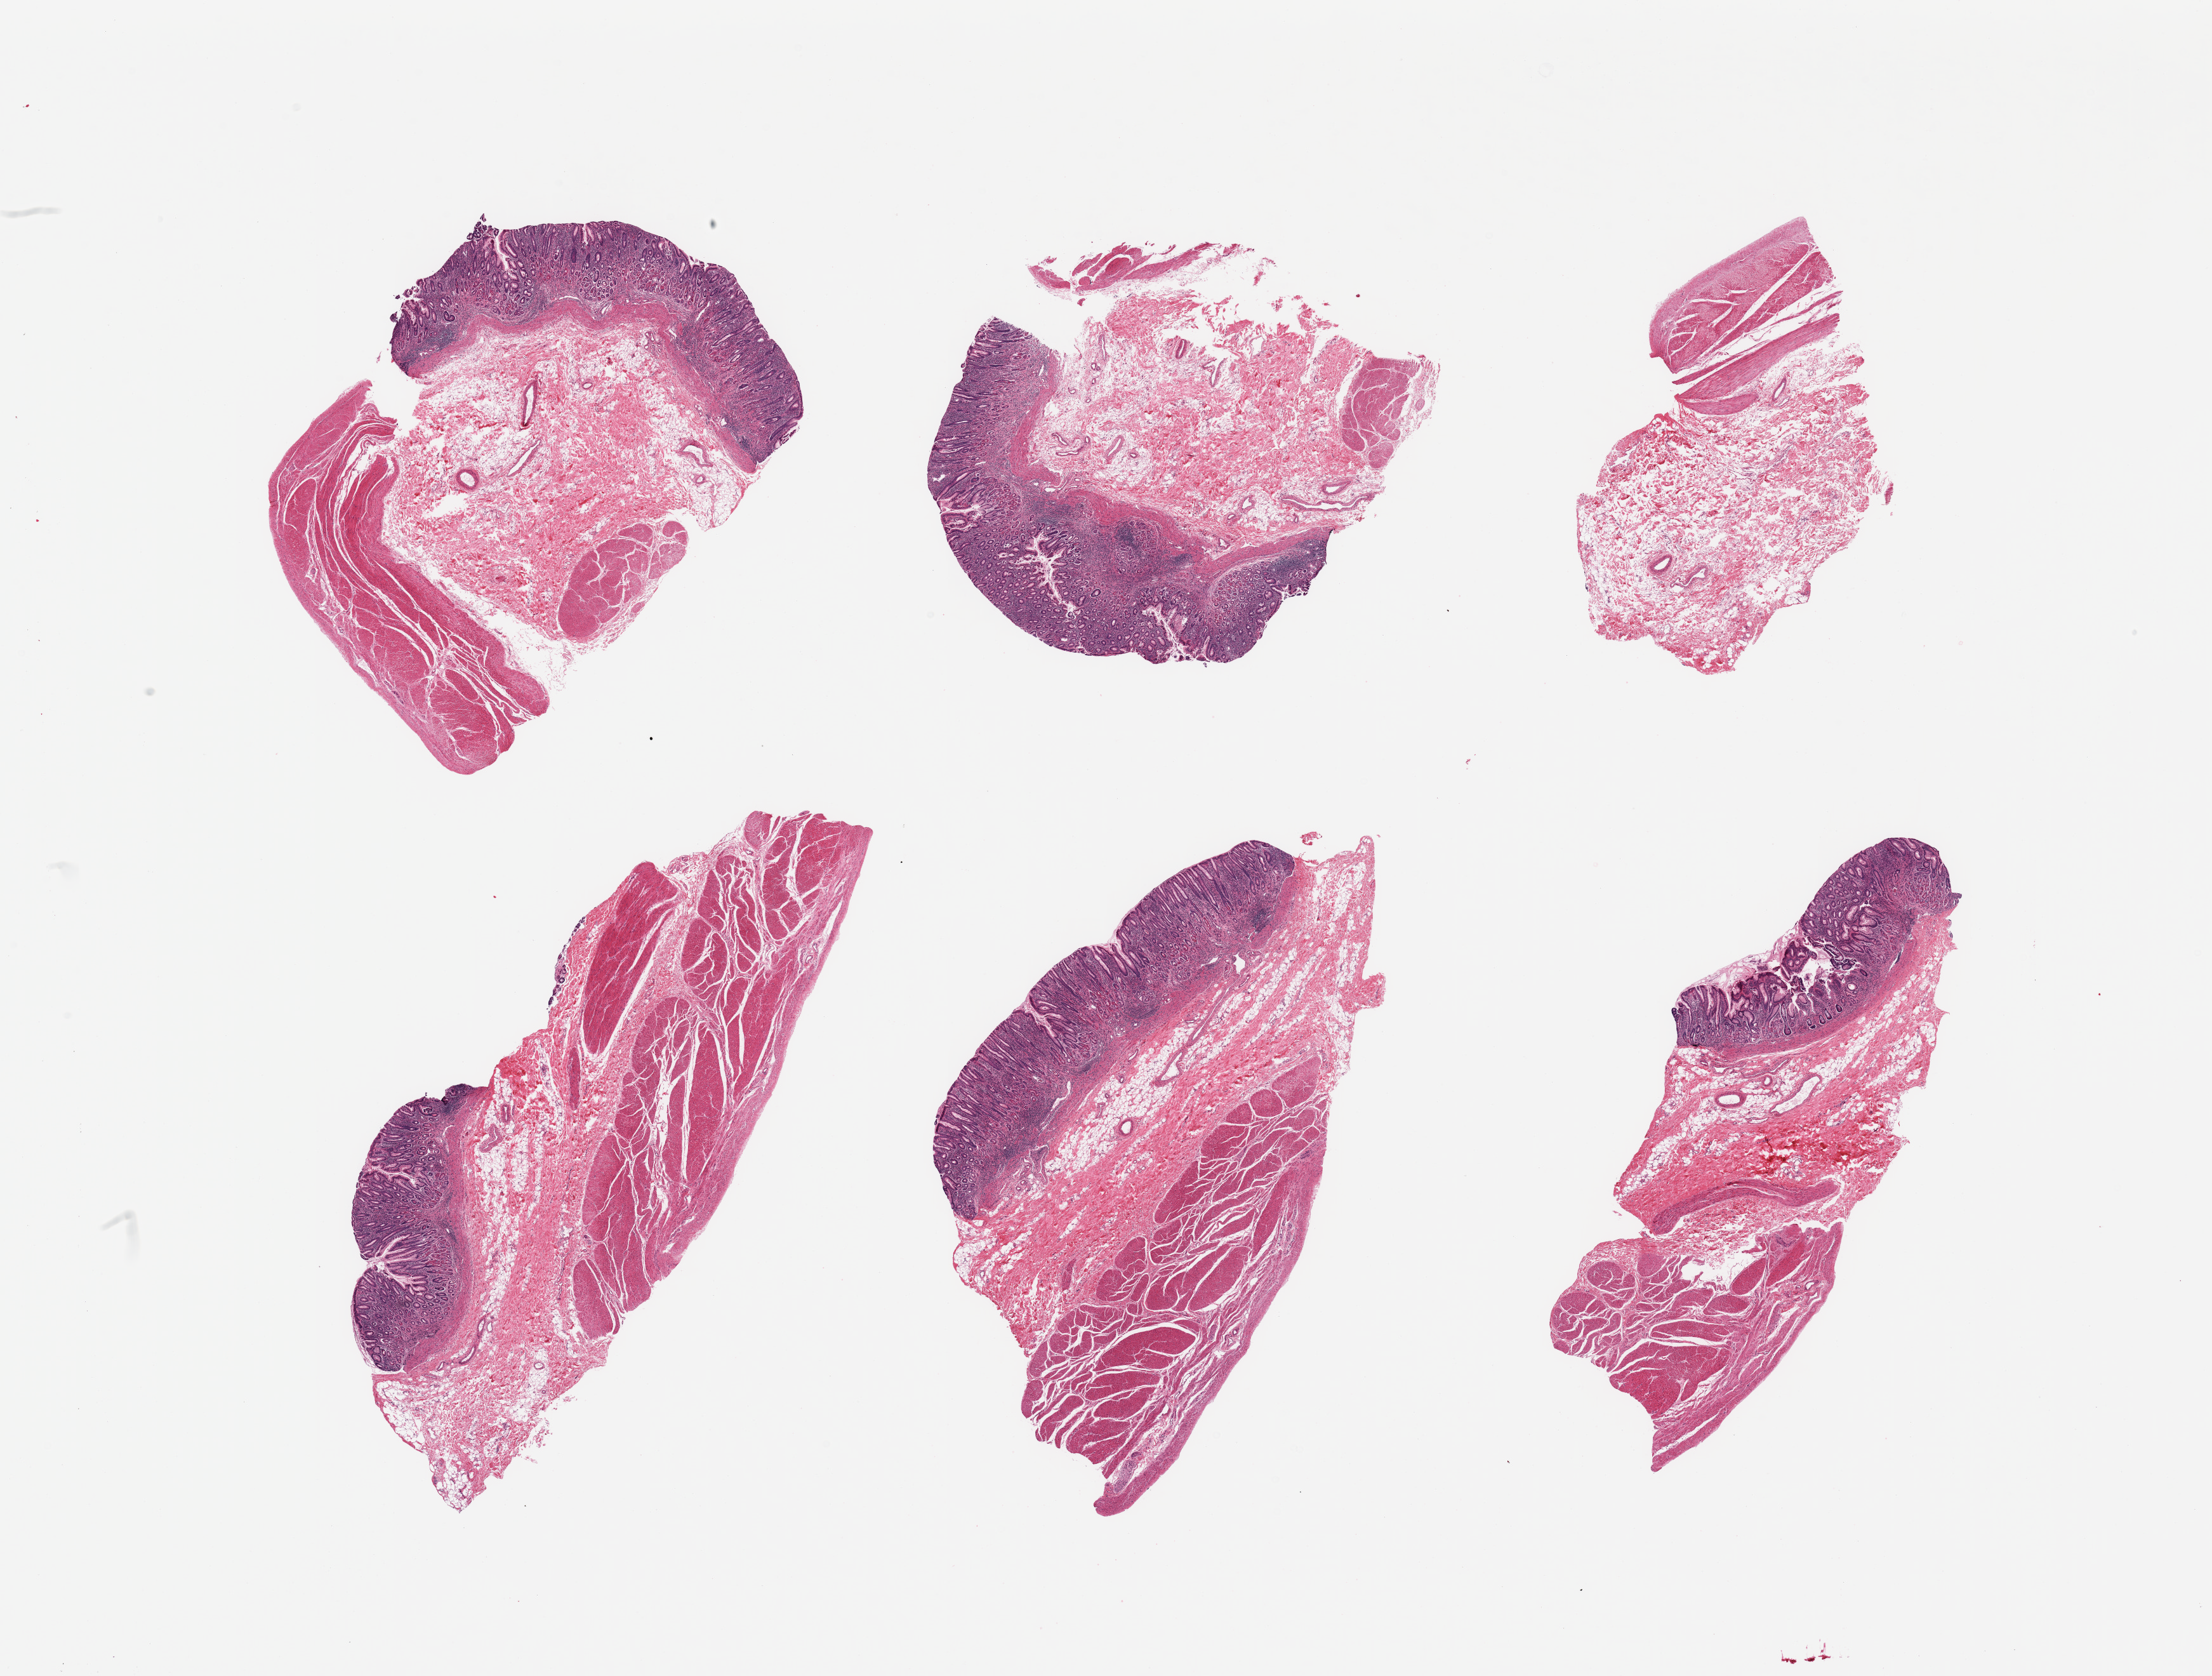
Whole-slide image, H&E stain, brightfield, shown as a low-resolution overview of the whole scanned area (about 27.6 x 20.9 mm, acquisition: 20x scan). PAXgene-fixed, paraffin-embedded tissue. Sampled site (target tissue): stomach. Tissue donor sample. Donor sex: male.
Review note (as recorded): 6 pieces, moderate chronic gastritis; mucosa up to ~1mm, ~25% thickness.